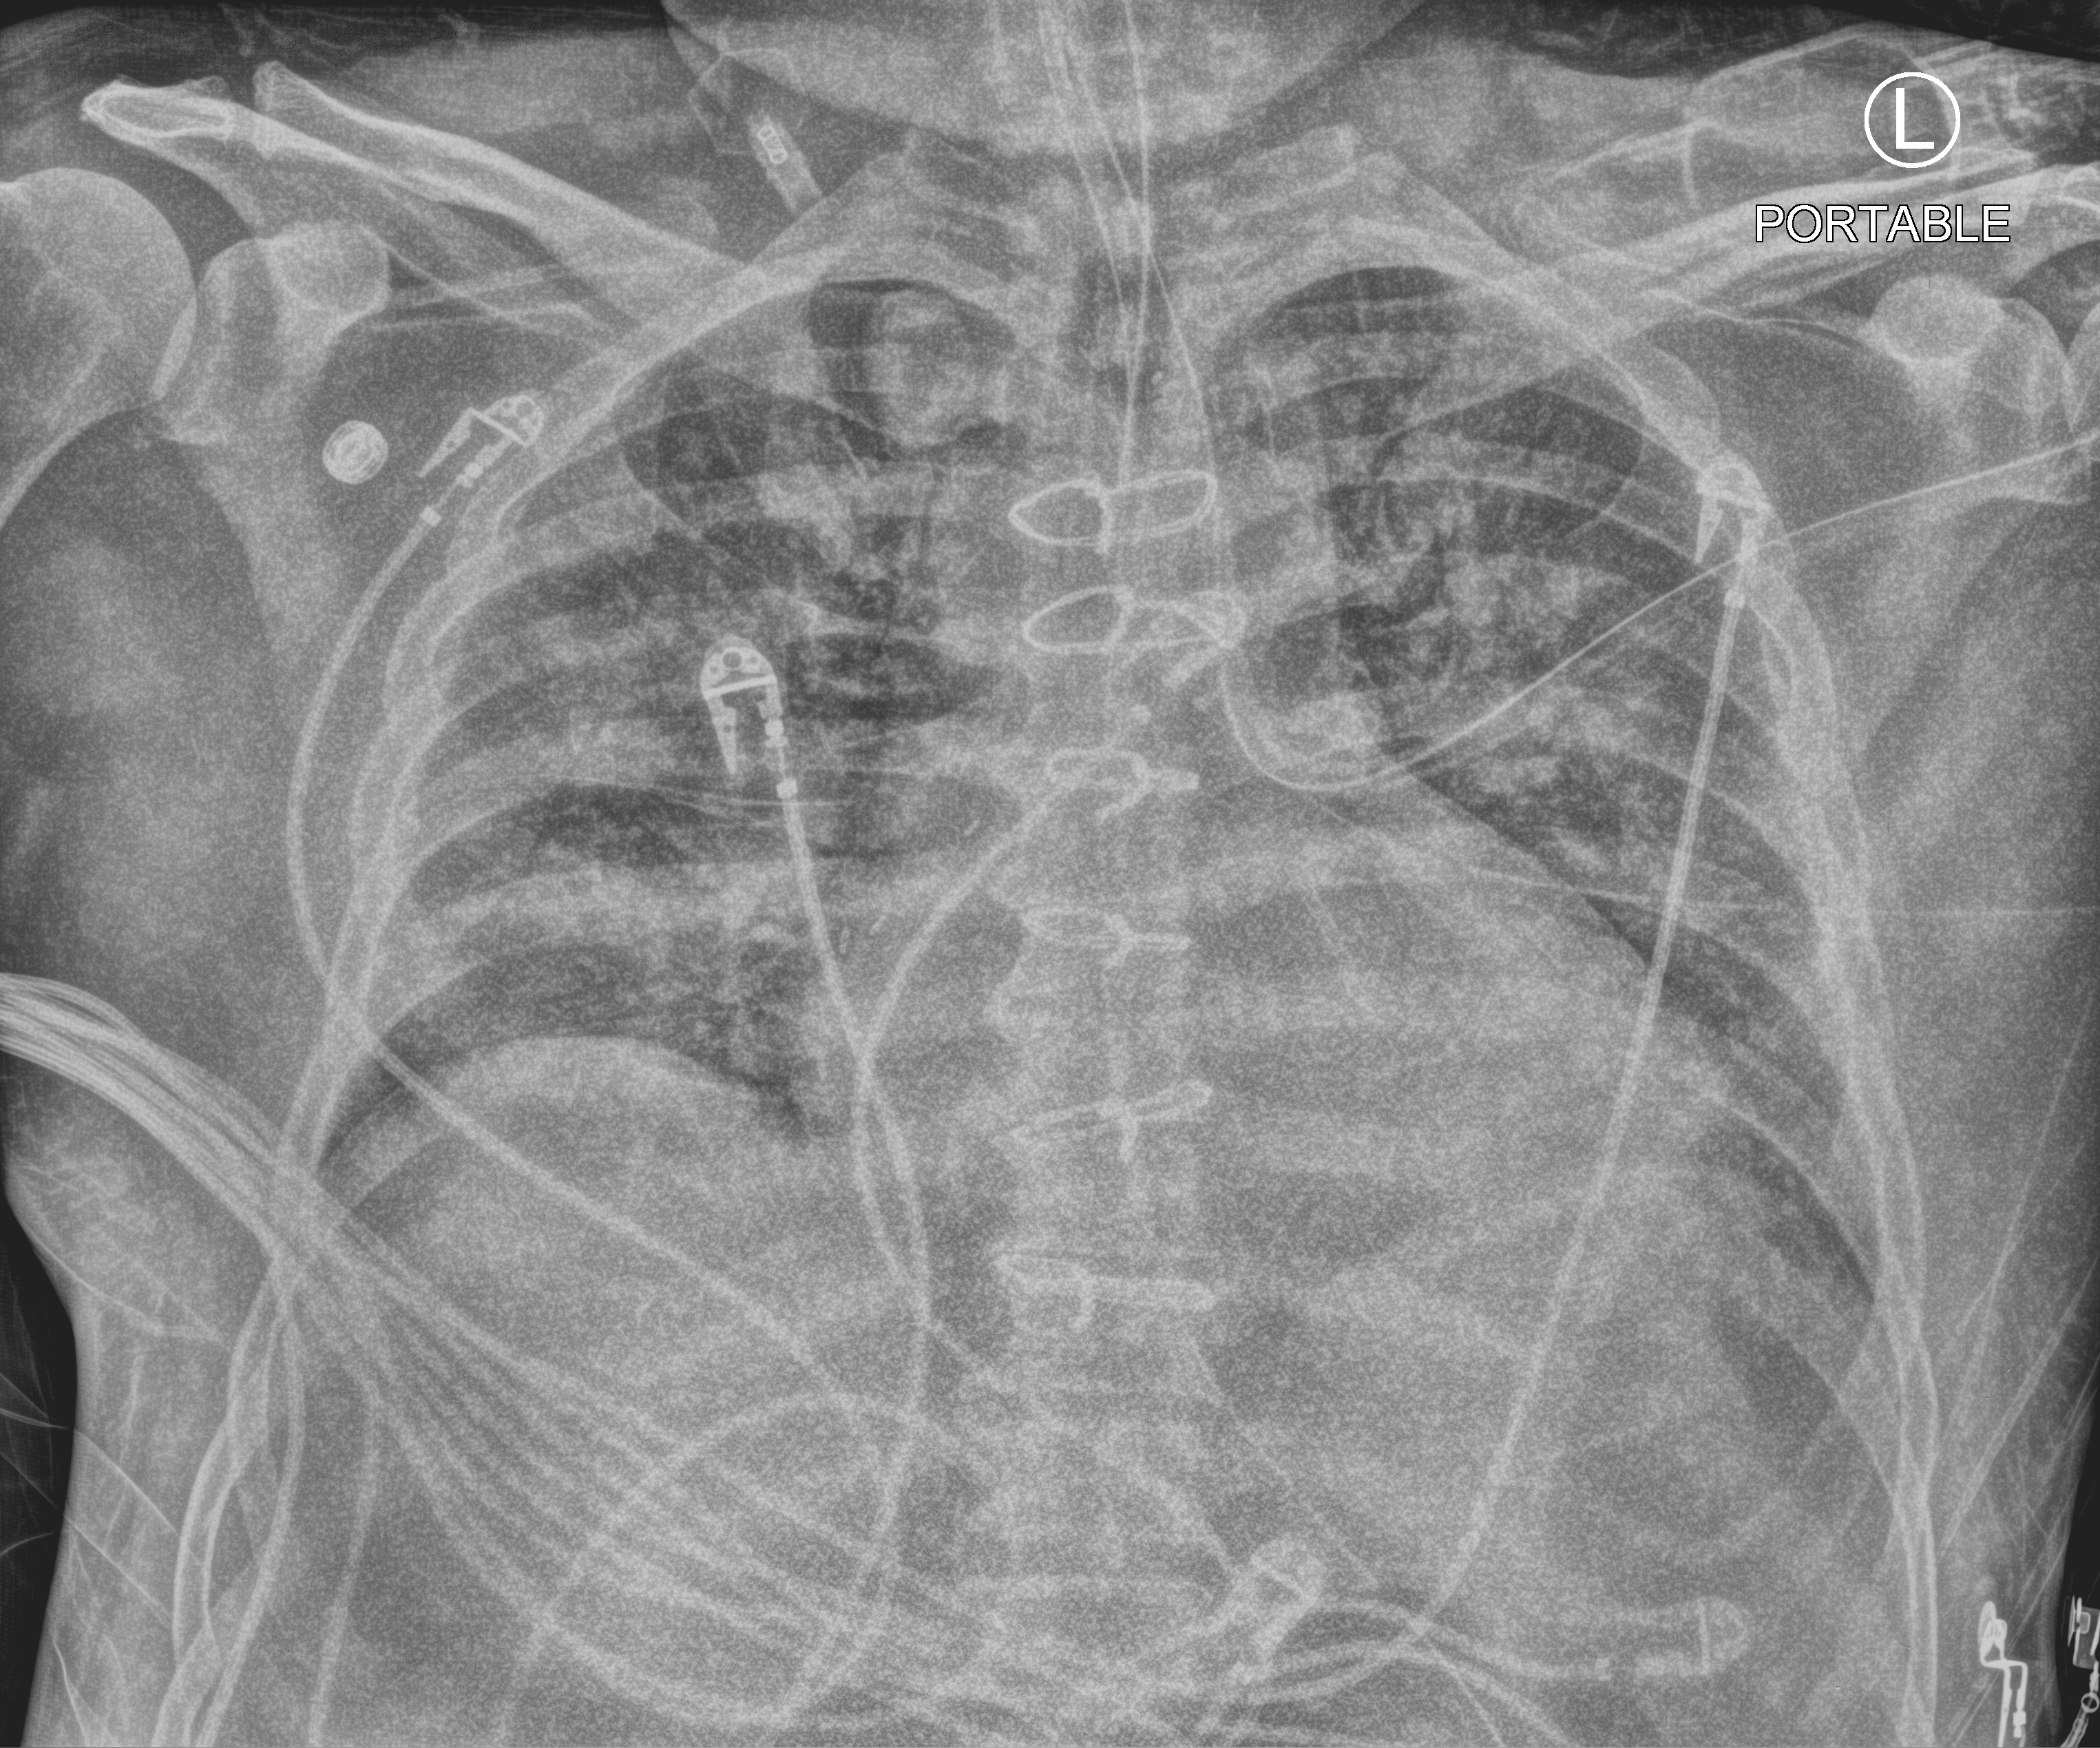
Chest X-ray (portable); anteroposterior (AP) projection. Adult patient hospitalised with COVID-19, age 18–59 years.
From the hospital-stay record, not from the radiograph (when in the stay this image was taken is not recorded):
- admitted to intensive care during this hospital stay: yes
- mechanically ventilated during this hospital stay: yes